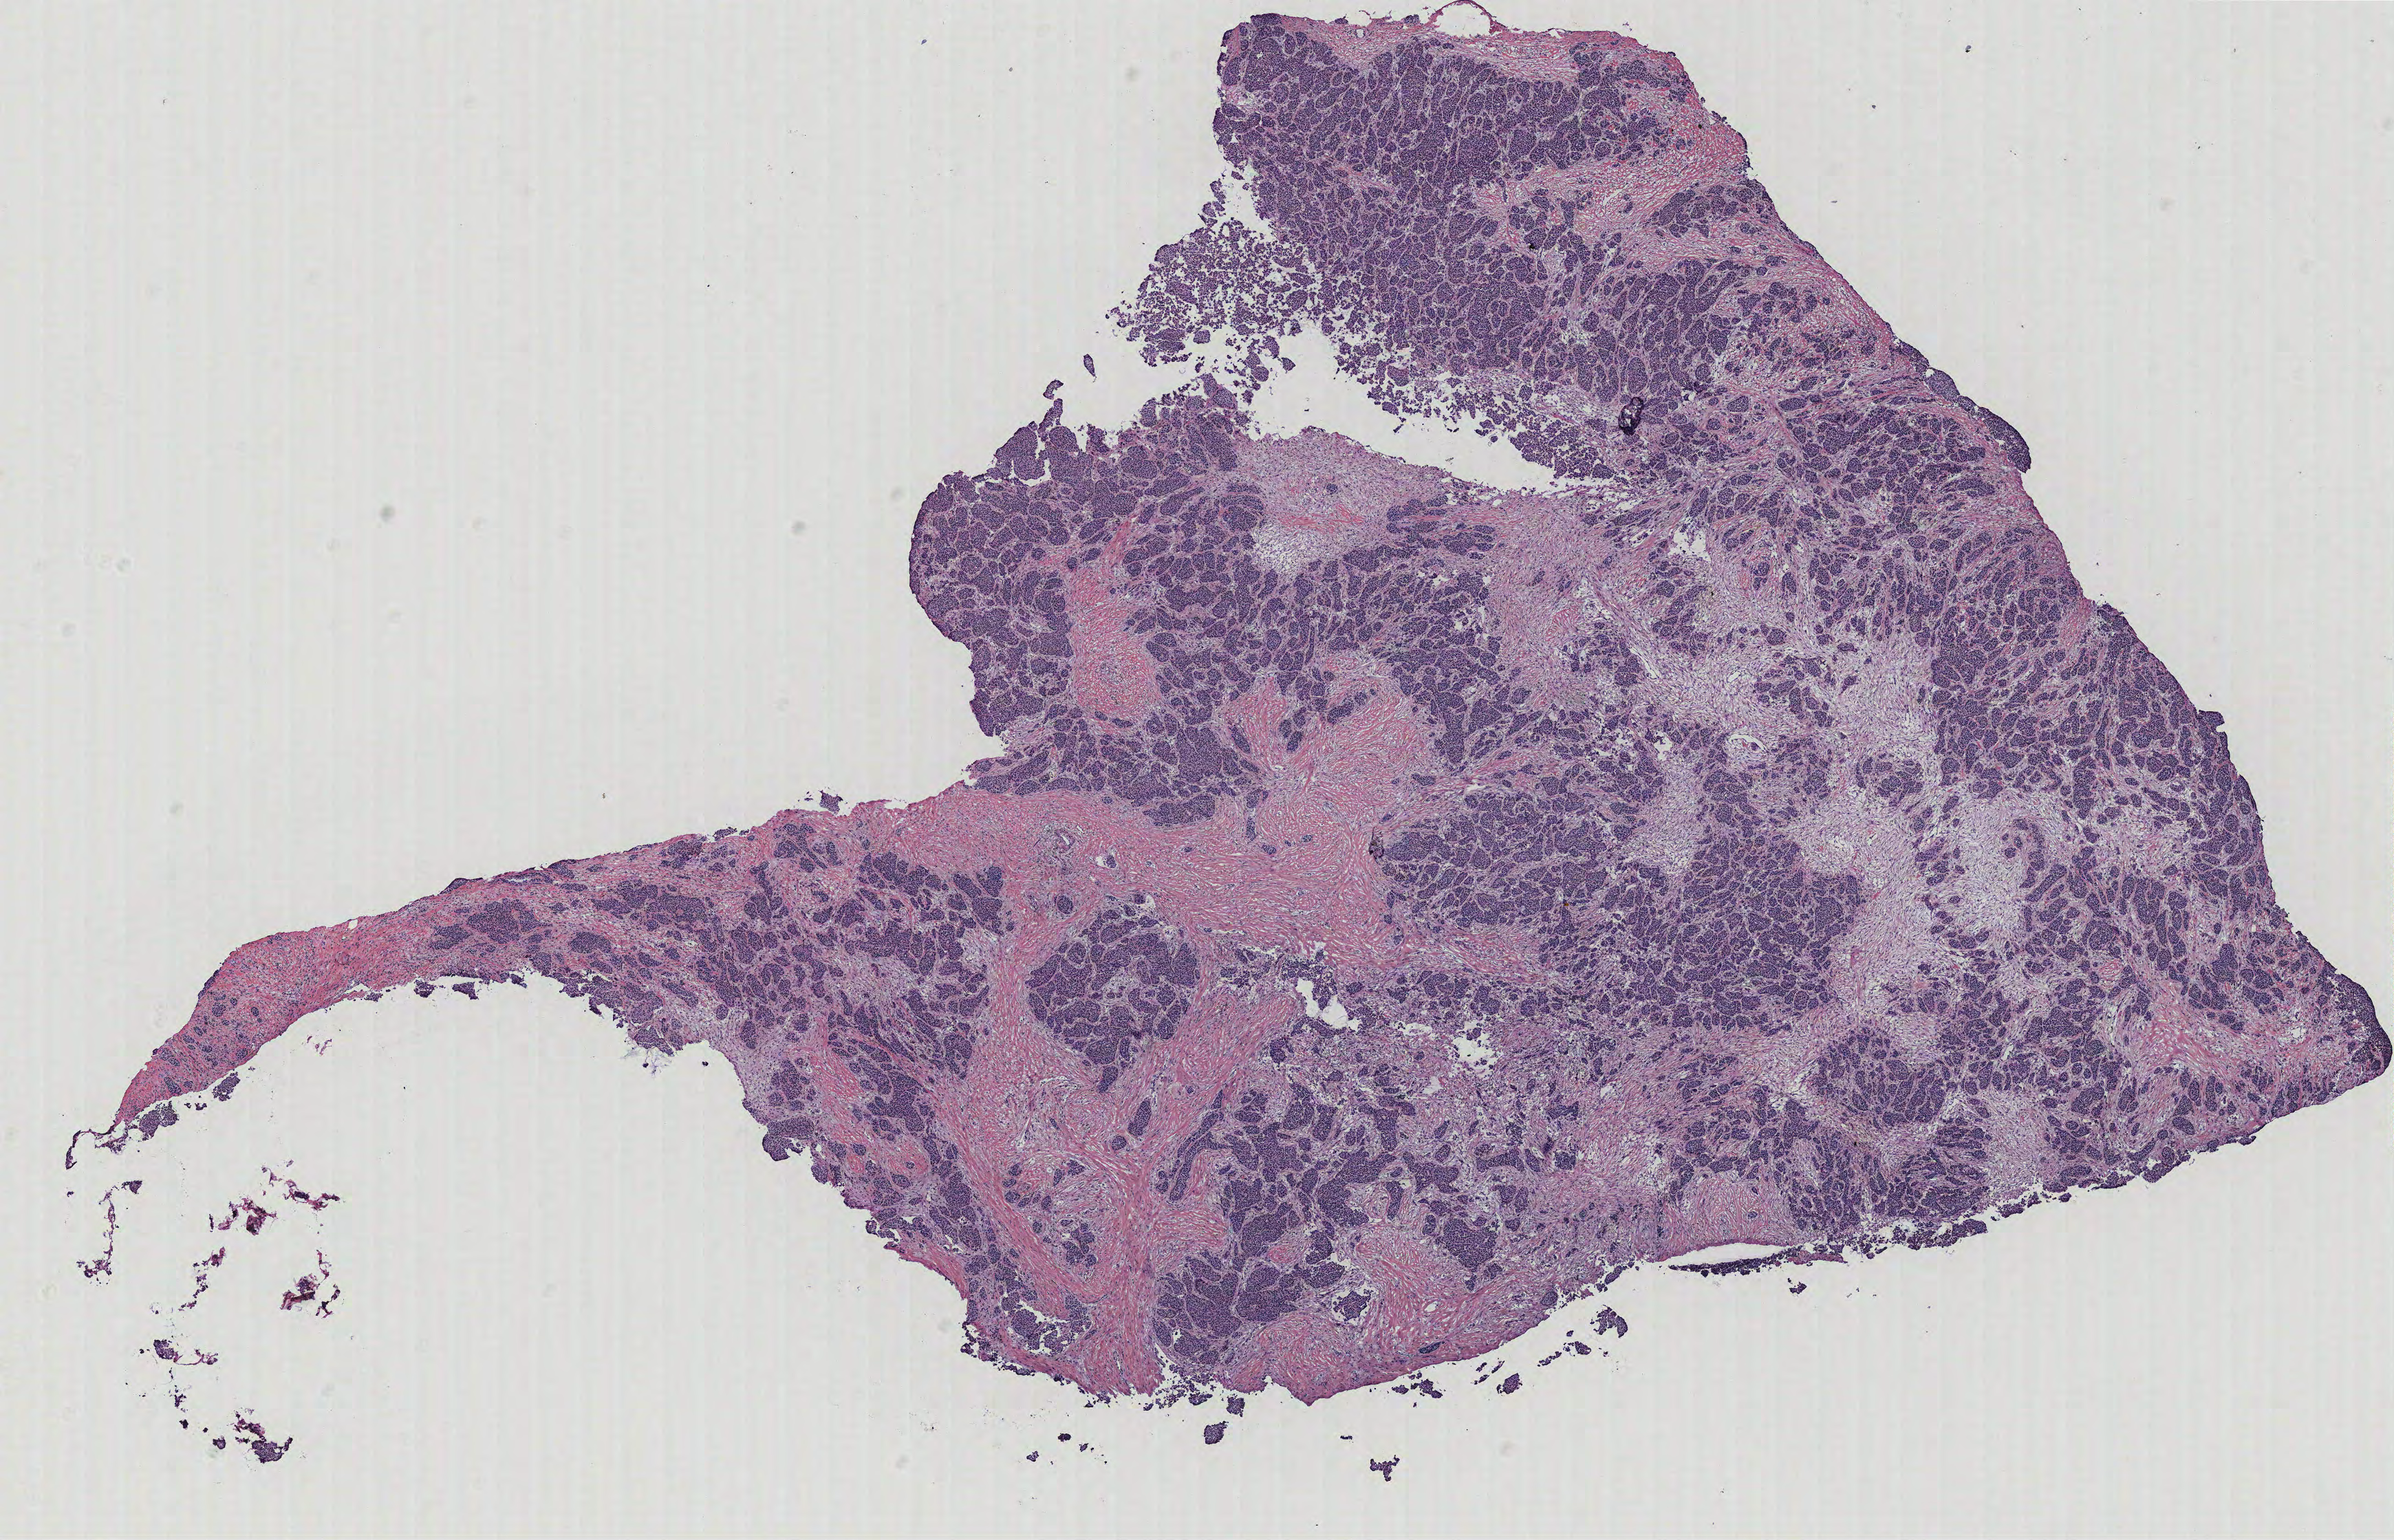
Whole-slide histology image, H&E-stained — low-resolution overview of the scanned area, about 13.9 x 9.0 mm (acquisition: 40x scan); breast, tissue type not recorded.
Patient diagnosis (cohort enrolment): breast cancer (breast).